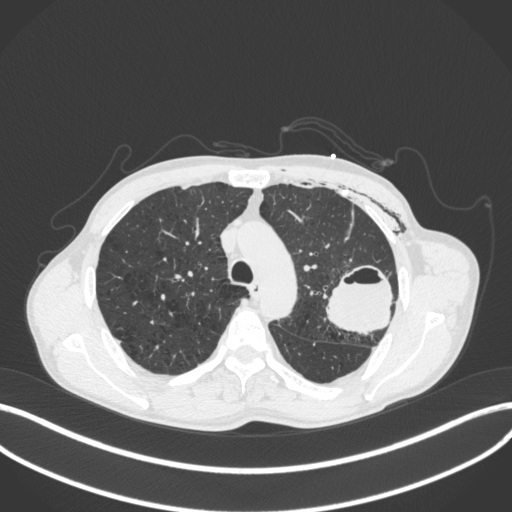
Chest CT, one axial slice. Slice 292 of 416 in the series (ordered by position). Reconstruction kernel B31f. 120 kVp. Lung window (W 1500 / L -600 HU). 512 × 512 image matrix. Male patient, age 58 years. Case-level facts recorded for this patient, not image findings: clinical TNM (as recorded): T3 N0 M0.
Structures marked on this image (bounding box drawn by a radiologist):
- lung tumour (recorded histology: adenocarcinoma): bounding box (x1, y1, x2, y2) in pixels: (324, 262, 398, 338)